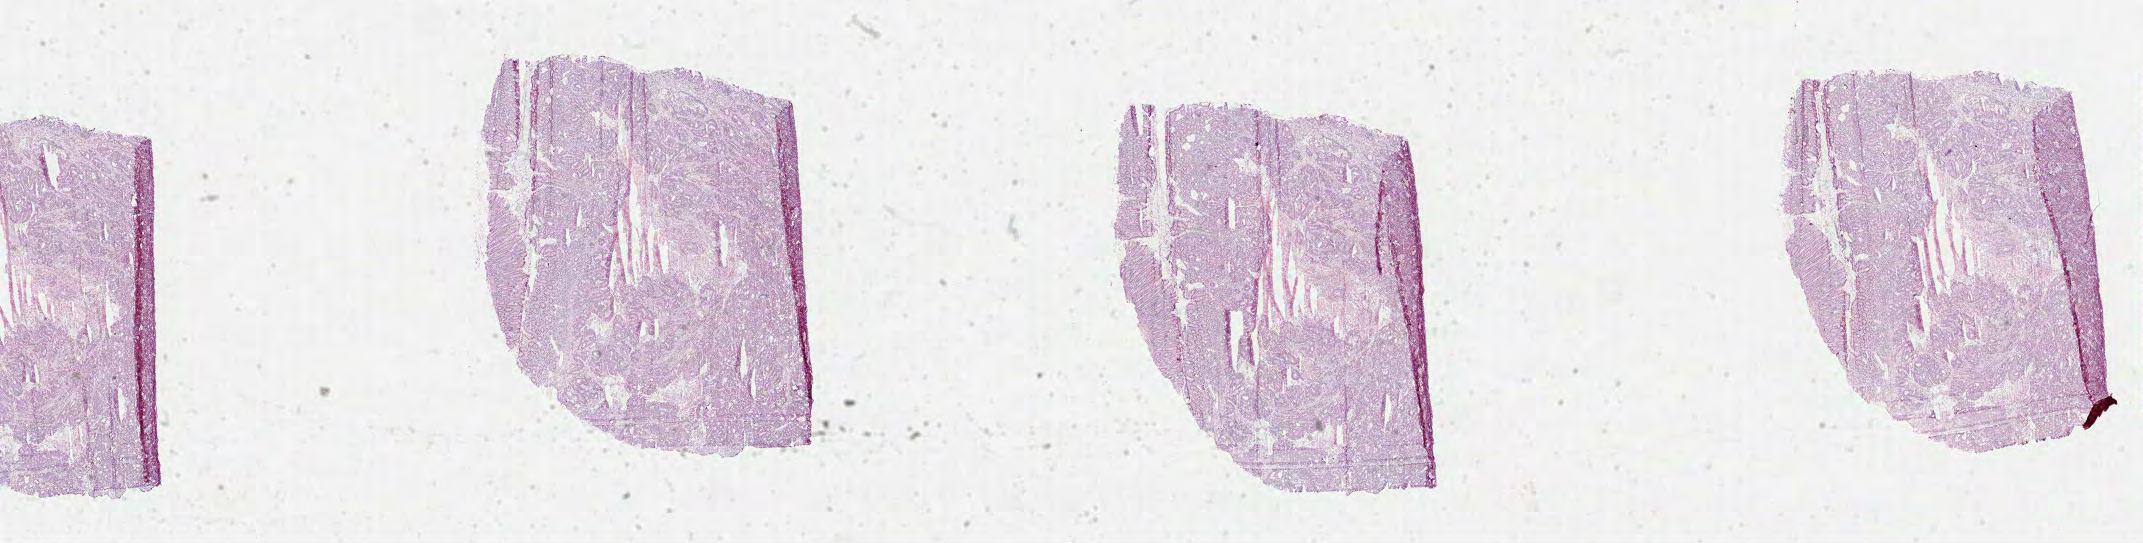
H&E whole-slide image, a low-resolution overview of the entire scanned area, about 34.6 x 8.8 mm; formalin-fixed paraffin-embedded (FFPE) diagnostic section; primary tumour sample from the colon. Male, age 77 years at initial diagnosis.
Diagnosis: Adenocarcinoma, NOS. Lymph nodes positive (case pathology): 4 of 14 examined. AJCC pathologic stage: IIIC.